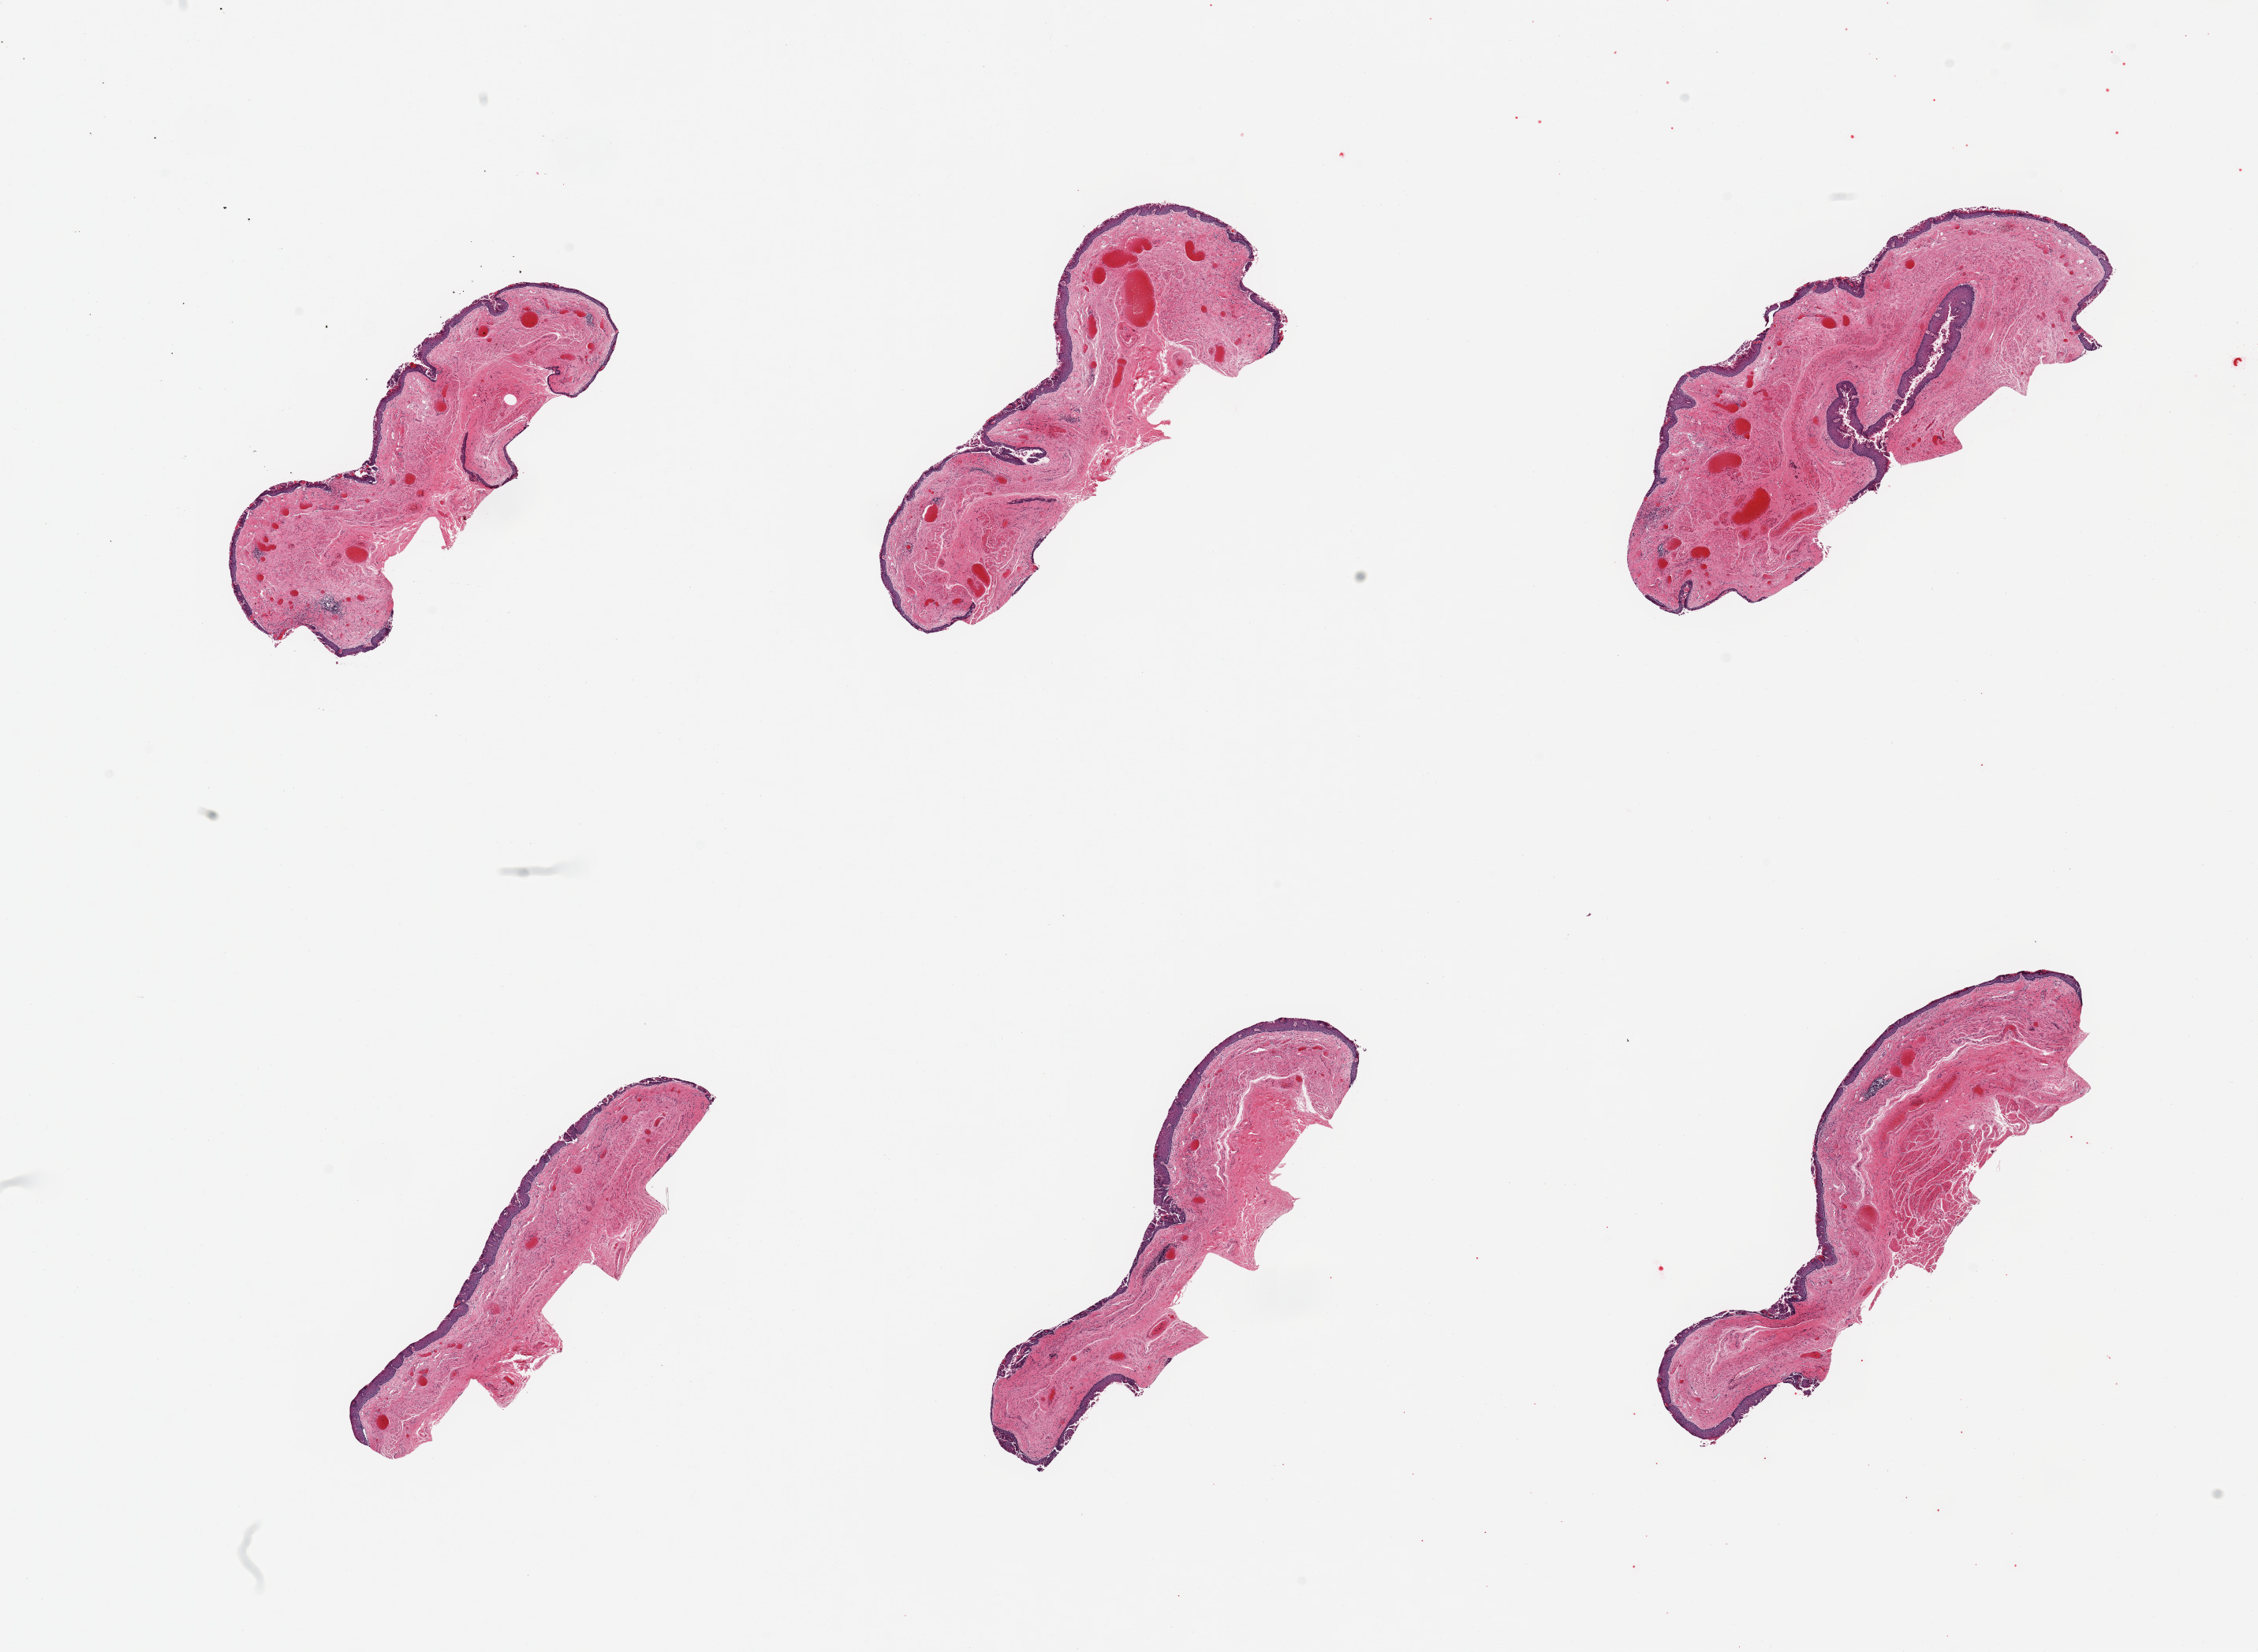
Digitized hematoxylin and eosin (H&E)-stained section, a low-resolution overview of the entire scanned area, about 22.6 x 16.6 mm (acquisition: 20x scan); PAXgene-fixed, paraffin-embedded tissue; section of esophageal mucous membrane (target tissue); donor tissue sample. Donor sex: male.
• review note (as recorded): 6 pieces; epithelial sloughing